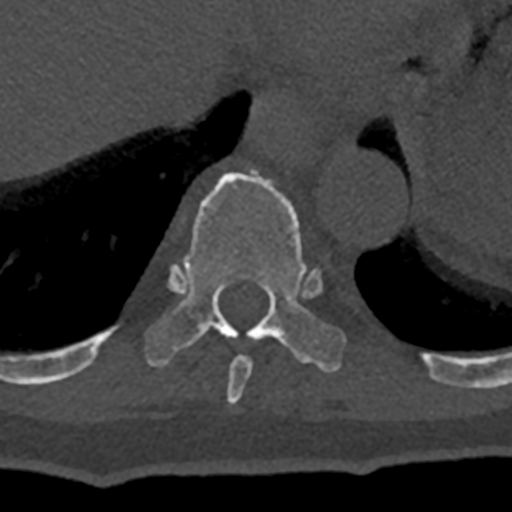
CT including the spine, one axial slice; slice 613 of 797 in the series (ordered by position); reconstruction kernel Br40s/3; bone window (W 1800 / L 400 HU); 512 × 512 image matrix. Male patient, age 74 years. Case-level facts recorded for this patient, not image findings: primary cancer: renal.
Outlined on this slice (semi-automatic segmentation, software-assisted and operator-edited):
- T10 vertebra: bounding box (x1, y1, x2, y2) in pixels: (70, 171, 432, 376)
- T9 vertebra: (226, 355, 252, 405)